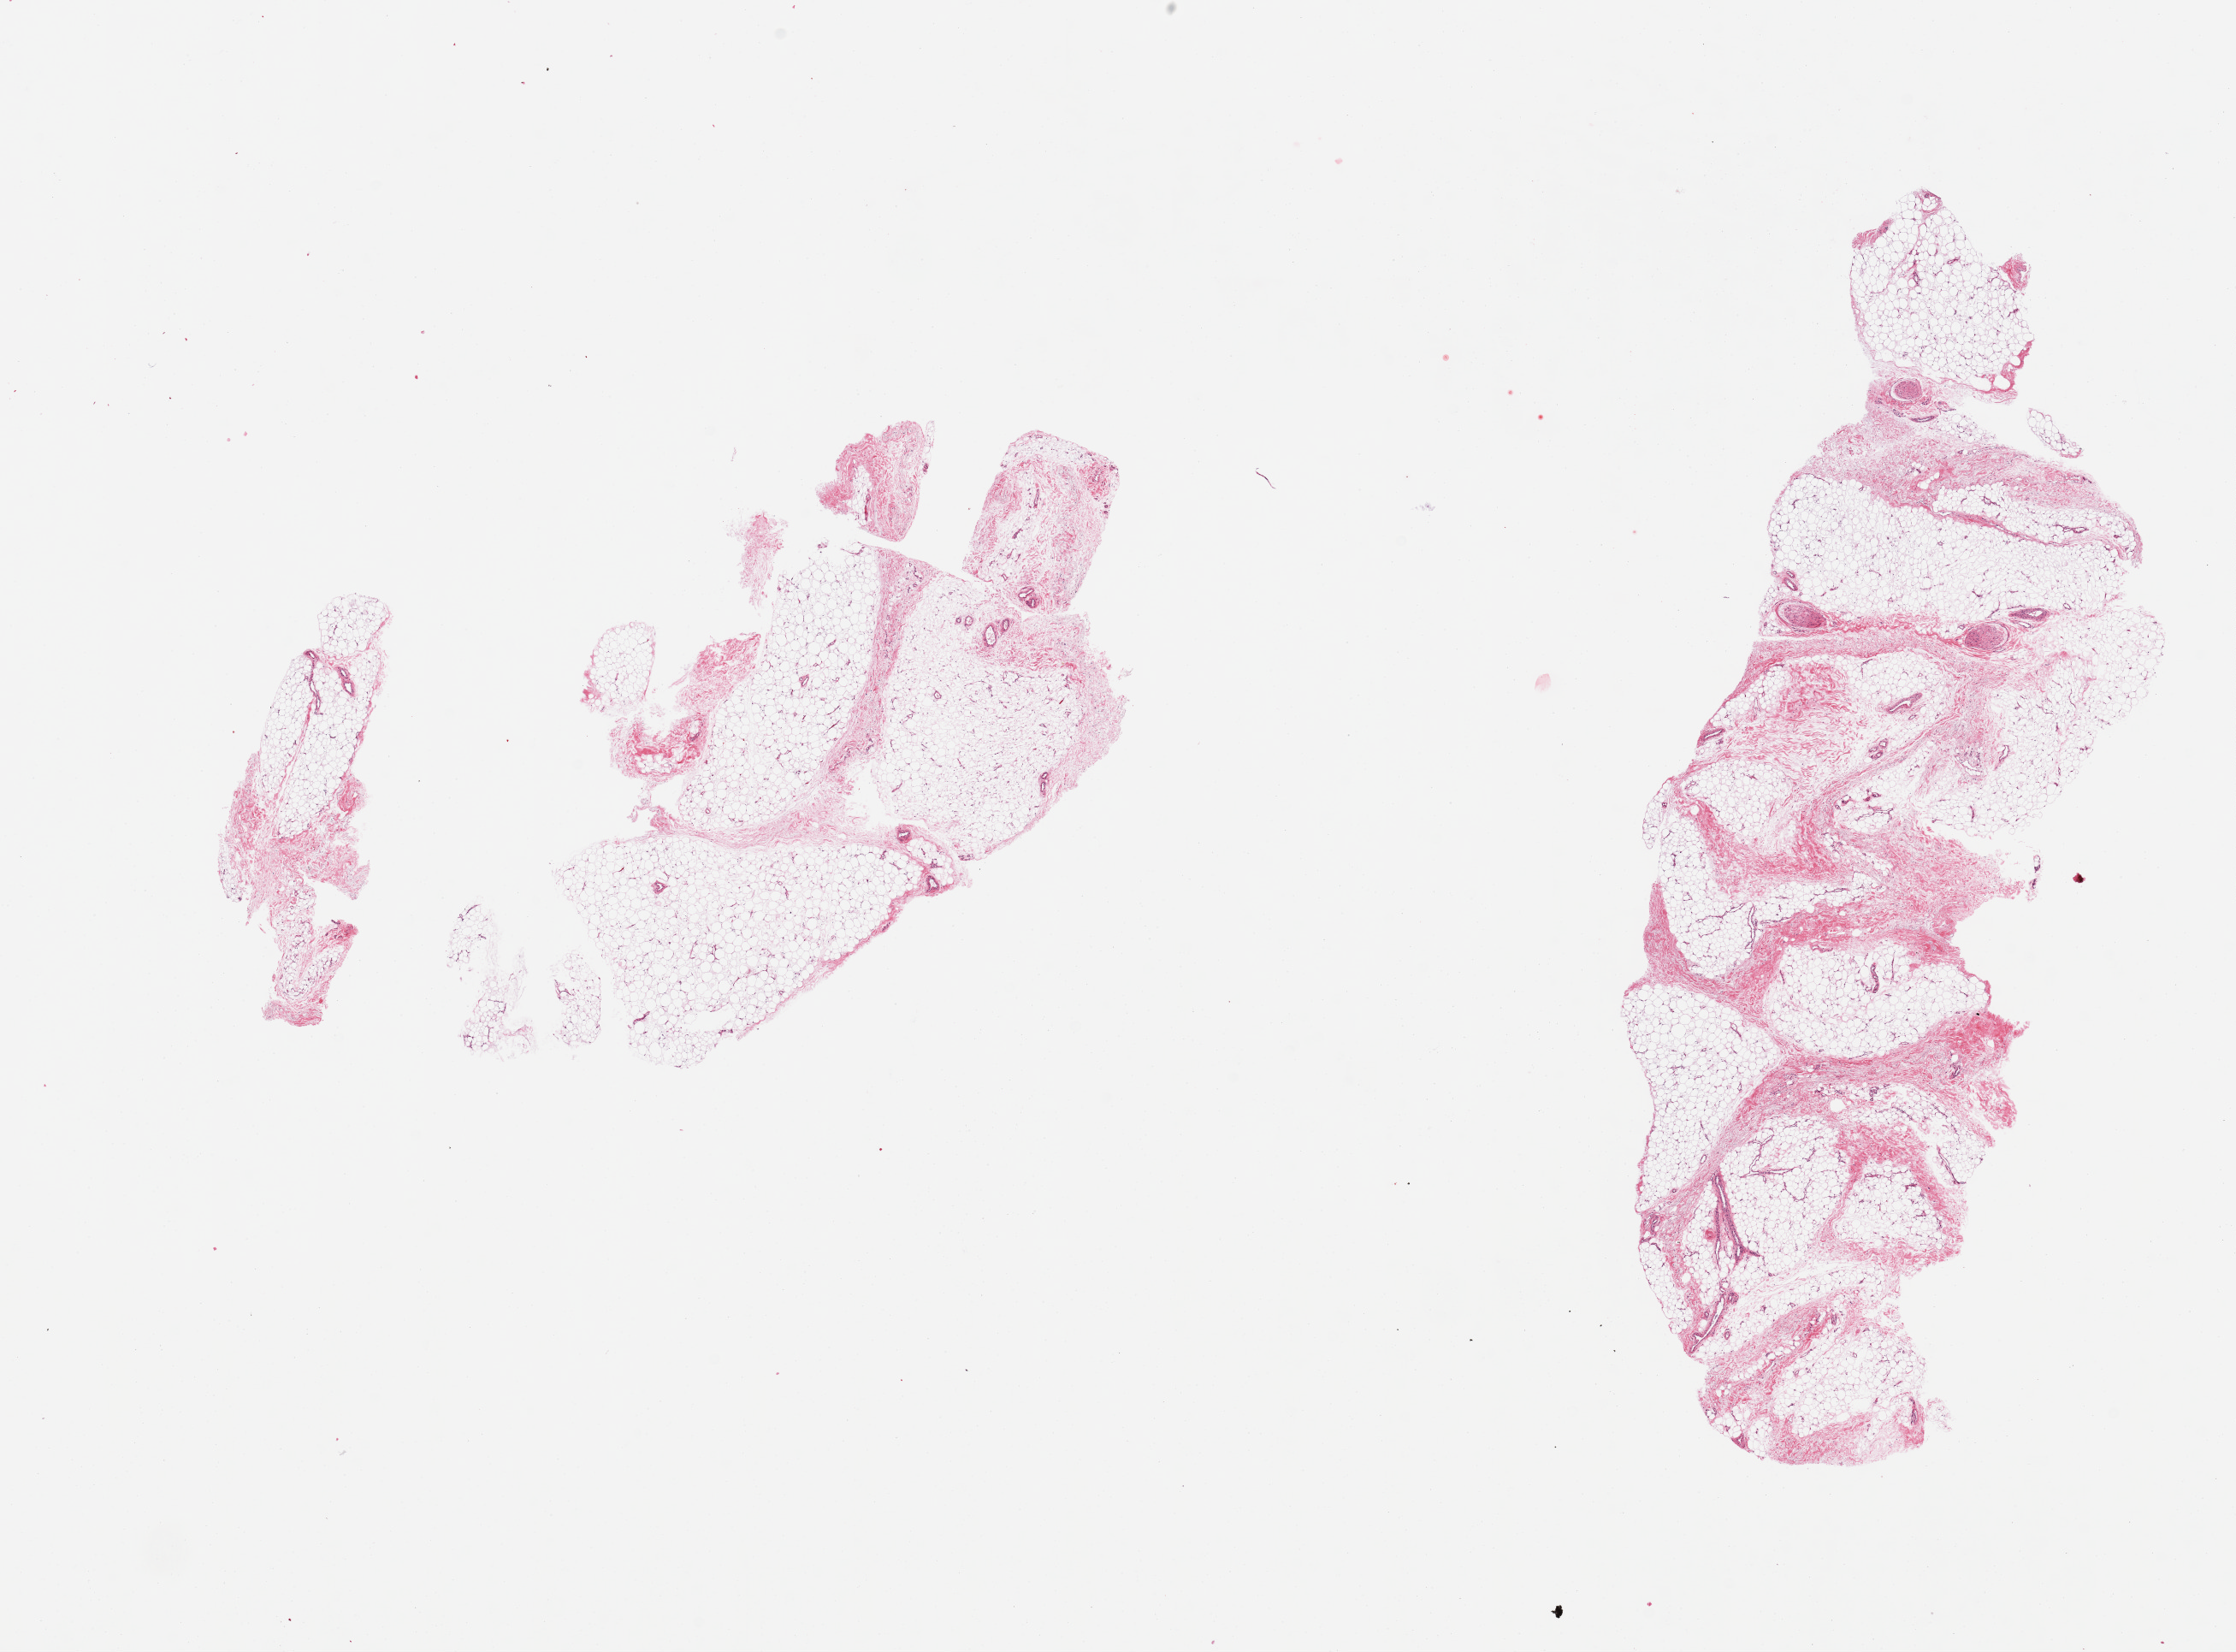
Digitized H&E-stained section, a low-resolution overview of the entire scanned area, about 20.7 x 15.3 mm; PAXgene-fixed, paraffin-embedded tissue; sampled site (target tissue): adipose tissue; tissue donor sample. Donor sex: male.
• review note (as recorded): 3 pieces; 20% fibrous component